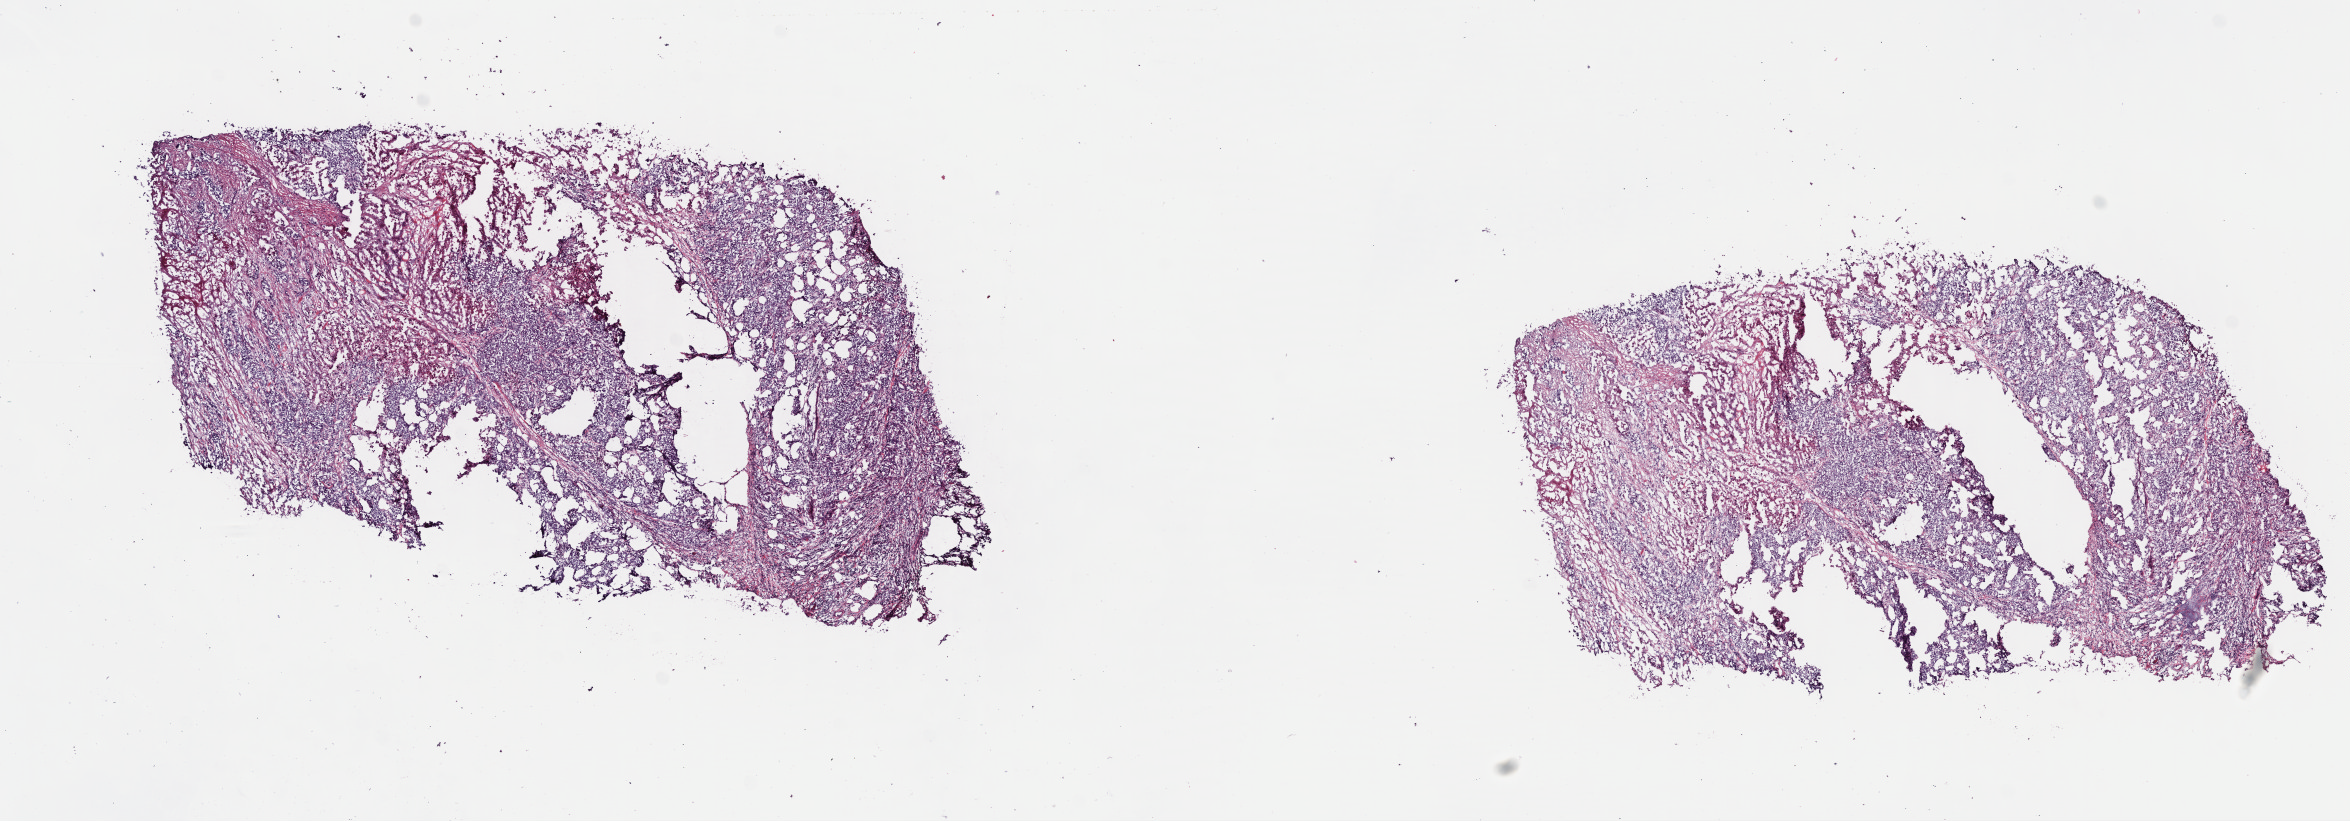
Digitized H&E-stained tissue section (whole slide) — low-resolution overview of the scanned area, about 18.5 x 6.5 mm, frozen section, lung, primary tumour sample. Female, age 44 years at initial diagnosis. Pathologist review of this section (percent, as recorded): tumour cells 50%, tumour nuclei 70%, normal cells 0%, stromal cells 30%, necrosis 20%. Infiltration values recorded for this section: lymphocyte infiltration 16%, monocyte infiltration 3%, neutrophil infiltration 3%.
• AJCC pathologic stage: III (6th edition)
• laterality: right
• diagnosis: Squamous cell carcinoma, NOS